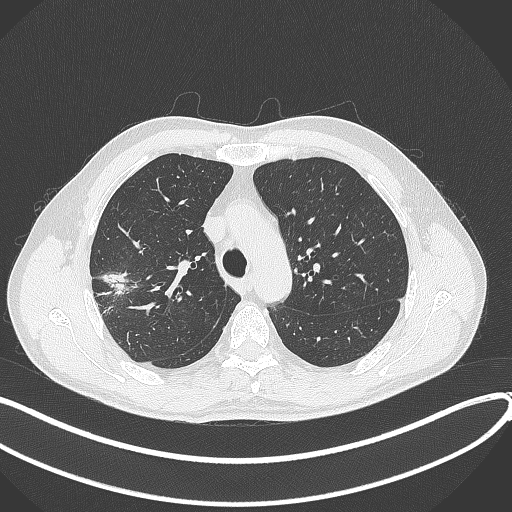
Chest CT, one axial slice; position 305 of 381 along the scan axis; 120 kVp; lung window (W 1500 / L -600 HU); 1 mm slice thickness; 512 × 512 image matrix, field of view 400 × 400 mm. Patient: male, 62 years. From the clinical record (not read from this slice): clinical TNM (as recorded): T1c N0 M0; histopathological grade: G2-3.
Annotated regions visible in this slice (rectangle marked by the reading radiologist):
- lung tumour (recorded histology: adenocarcinoma): bounding box <101,264,129,296> (left, top, right, bottom; pixels)